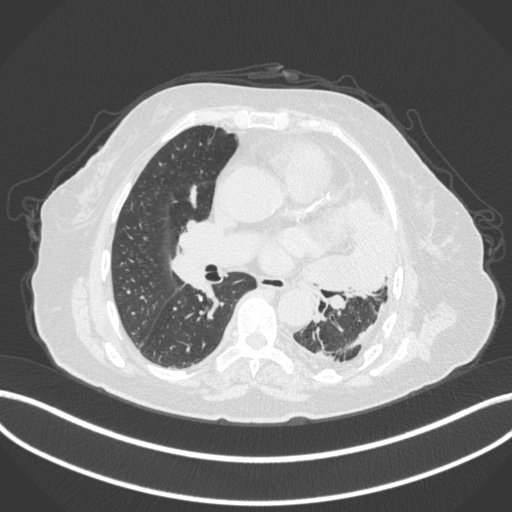
Chest CT, one axial slice. Position 193 of 399 along the scan axis. Reconstruction kernel B31f. 120 kVp. Lung window (W 1500 / L -600 HU). 1 mm slice thickness. 512 × 512 image matrix. Female patient, age 75 years. From the clinical record (not read from this slice): clinical TNM (as recorded): T3 N3 M1.
Structures marked on this image (bounding box drawn by a radiologist):
- lung tumour (recorded histology: adenocarcinoma): bounding box (x1, y1, x2, y2) in pixels: (298, 198, 399, 302)